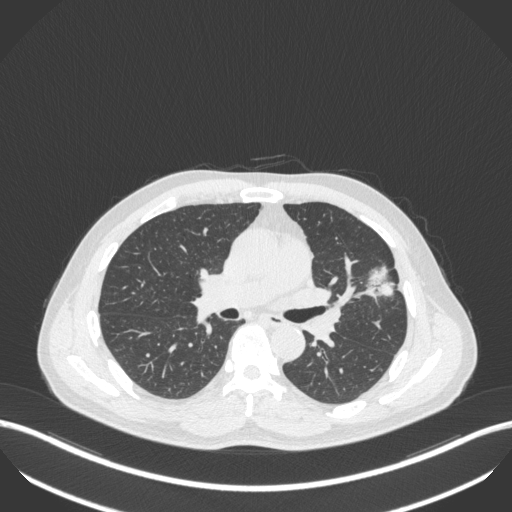
Chest CT, one axial slice; position 228 of 418 along the scan axis; reconstruction kernel B31f; lung window (W 1500 / L -600 HU); 1 mm slice thickness; 512 × 512 image matrix, field of view 400 × 400 mm. Patient: male, 55 years. Case-level facts recorded for this patient, not image findings: clinical TNM (as recorded): T1c N0 M0; histopathological grade: G2-3.
Annotated regions visible in this slice (rectangle marked by the reading radiologist):
- lung tumour (recorded histology: adenocarcinoma): bounding box <358,265,396,299> (left, top, right, bottom; pixels)